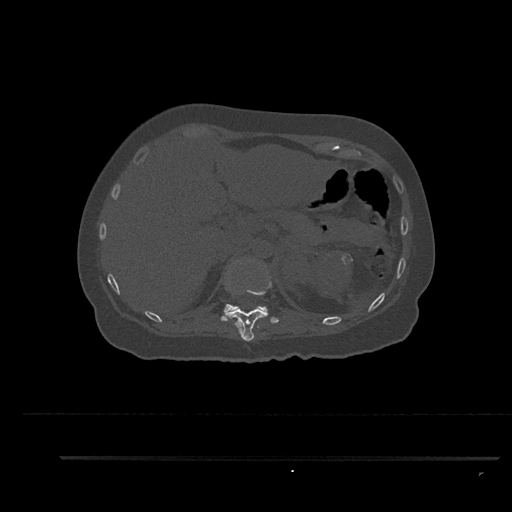
CT including the spine, one axial slice. Position 295 of 797 along the scan axis. Reconstruction kernel Br40s/3. 120 kVp. Bone window (W 1800 / L 400 HU). 0.5 mm slice thickness. 512 × 512 image matrix, field of view 408 × 408 mm. Female patient, age 44 years. From the clinical record (not read from this slice): primary cancer: renal; vertebrae with lytic lesions (as recorded): L1.
Structures marked on this image (semi-automatically segmented with operator editing):
- T11 vertebra: bounding box (x1, y1, x2, y2) in pixels: (229, 262, 272, 341)
- T12 vertebra: (220, 259, 269, 321)